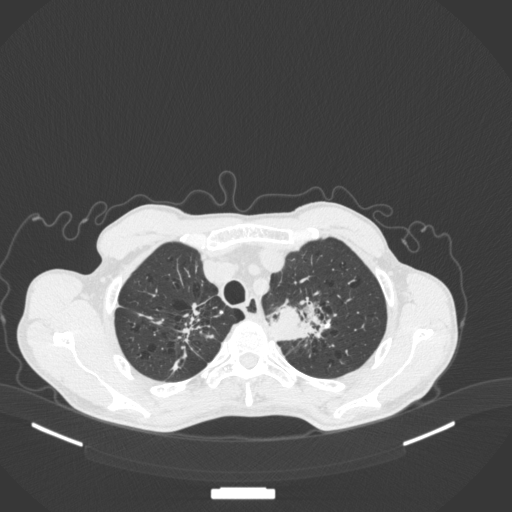
Chest CT, one axial slice. Position 358 of 394 along the scan axis. Reconstruction kernel B31f. Lung window (W 1500 / L -600 HU). 1 mm slice thickness. 512 × 512 image matrix. Patient: male, 65 years. Case-level facts recorded for this patient, not image findings: clinical TNM (as recorded): T2b N0 M0; histopathological grade: G2.
Annotated regions visible in this slice (rectangle marked by the reading radiologist):
- lung tumour (recorded histology: adenocarcinoma): box from (x=265, y=294) to (x=333, y=338) px